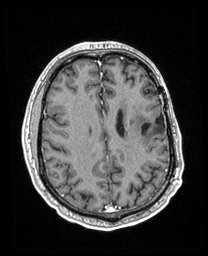
Brain MRI from a brain-tumour surgery series, one axial slice. T1-weighted post-contrast. 208 × 256 image matrix. From the clinical record (not read from this slice): histopathology: Astrocytoma; WHO grade: 3.
Annotated regions visible in this slice (manually delineated by an expert):
- previous resection cavity: bounding box <142,114,165,134> (left, top, right, bottom; pixels)